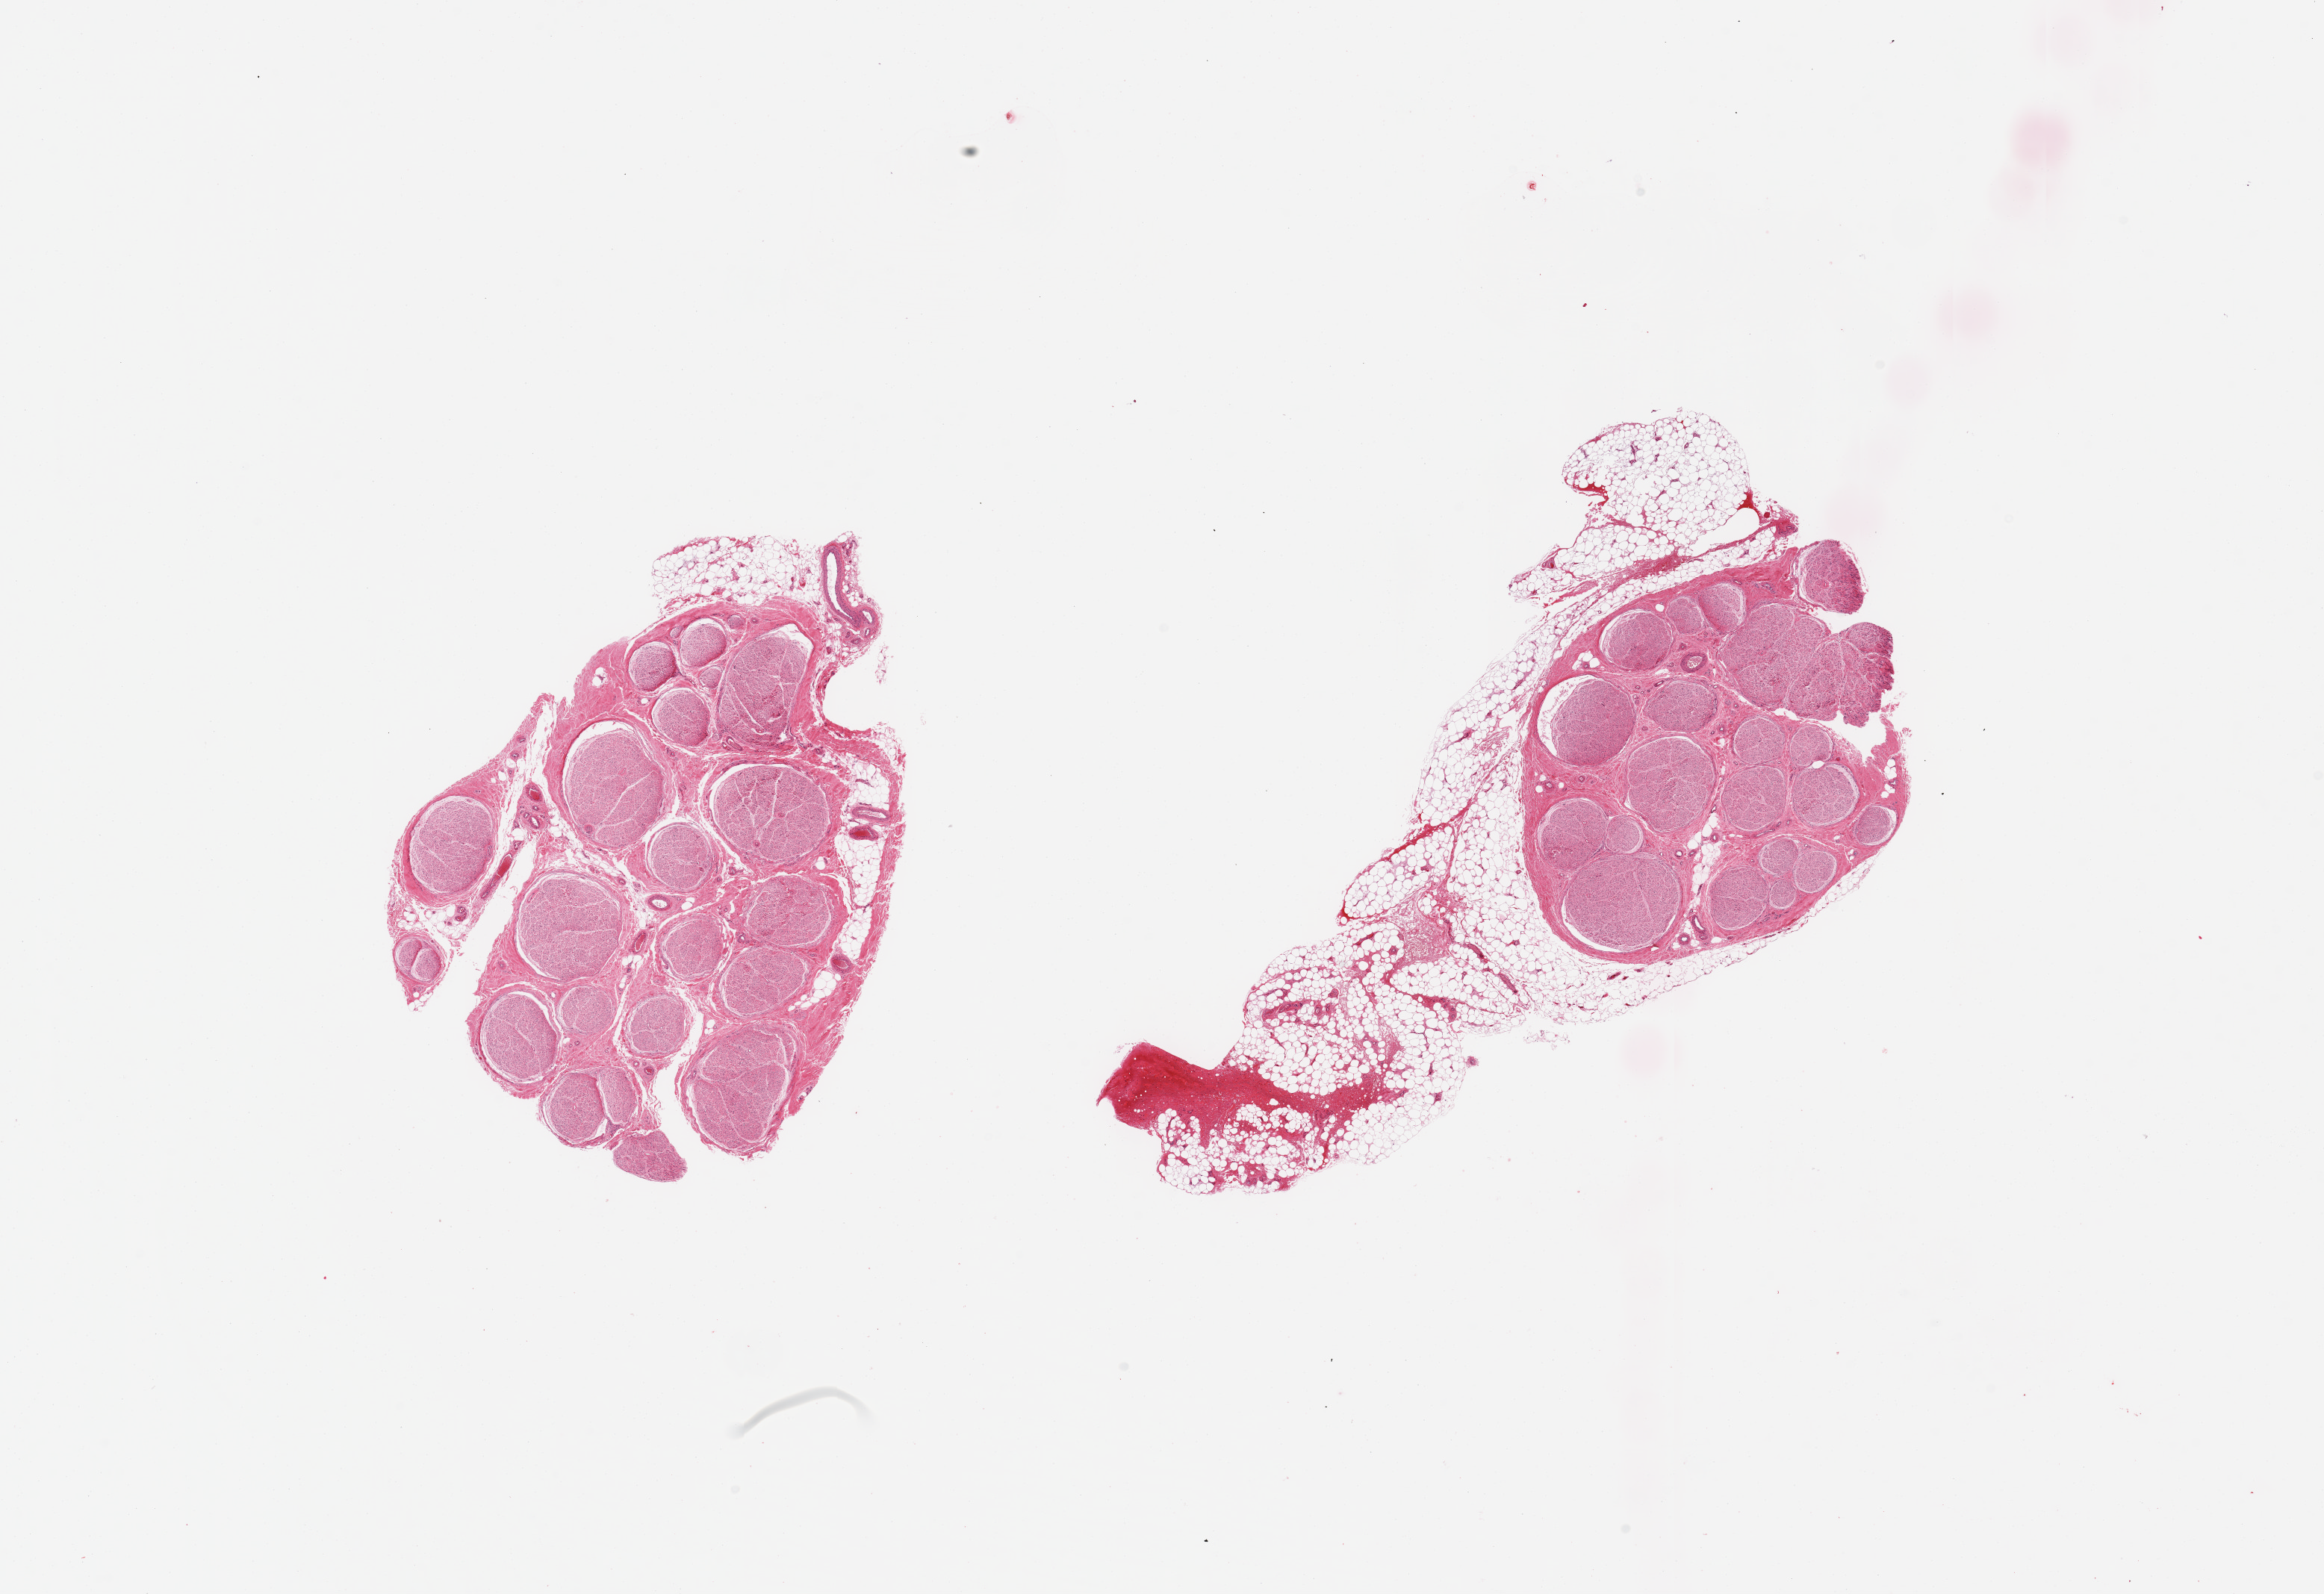
Whole-slide image, haematoxylin and eosin stain — low-resolution overview of the scanned area, about 24.6 x 16.9 mm (from a 20x scan), PAXgene-fixed paraffin-embedded (PFPE) section, section of tibial nerve (target tissue), tissue donor sample. Male donor.
* reviewer comment on this tissue sample: 2 pieces; 40% external fat on 1 piece